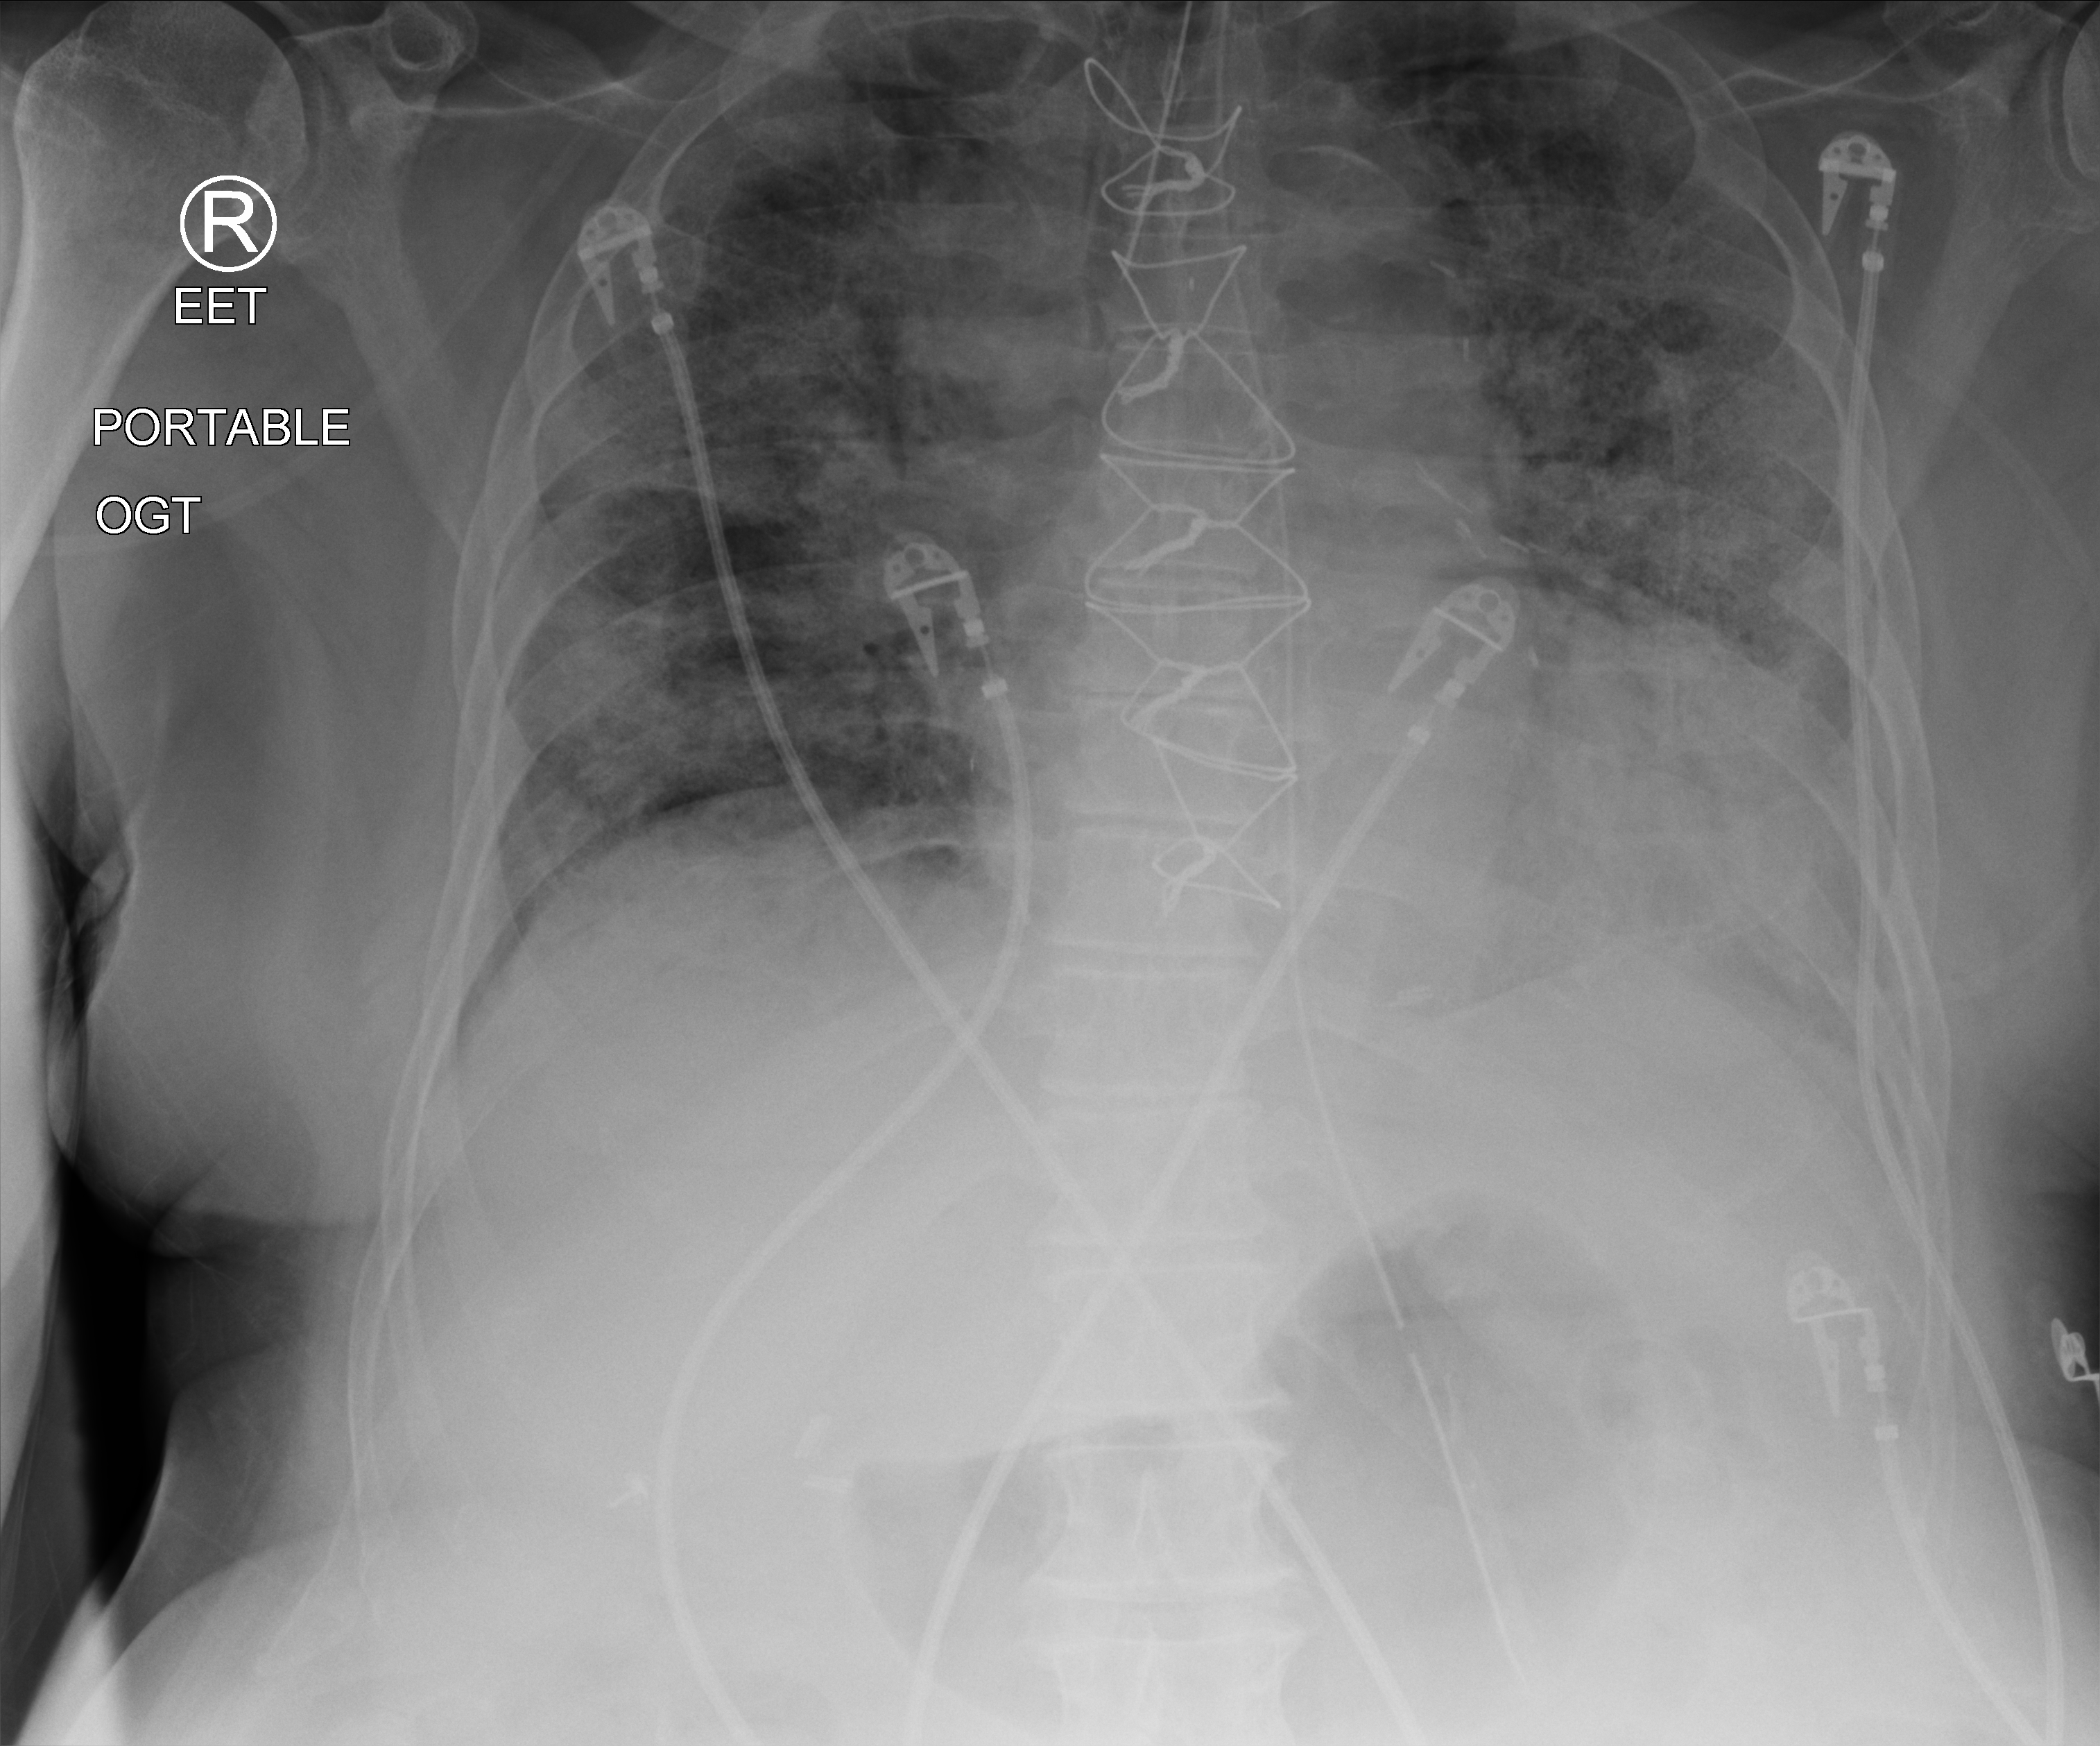
Chest X-ray (portable). Patient hospitalised with COVID-19; male, aged 75–90 years.
Admission-level facts for this patient (not findings on this image; timing relative to this image not recorded): mechanically ventilated during this hospital stay: yes; admitted to intensive care during this hospital stay: yes.